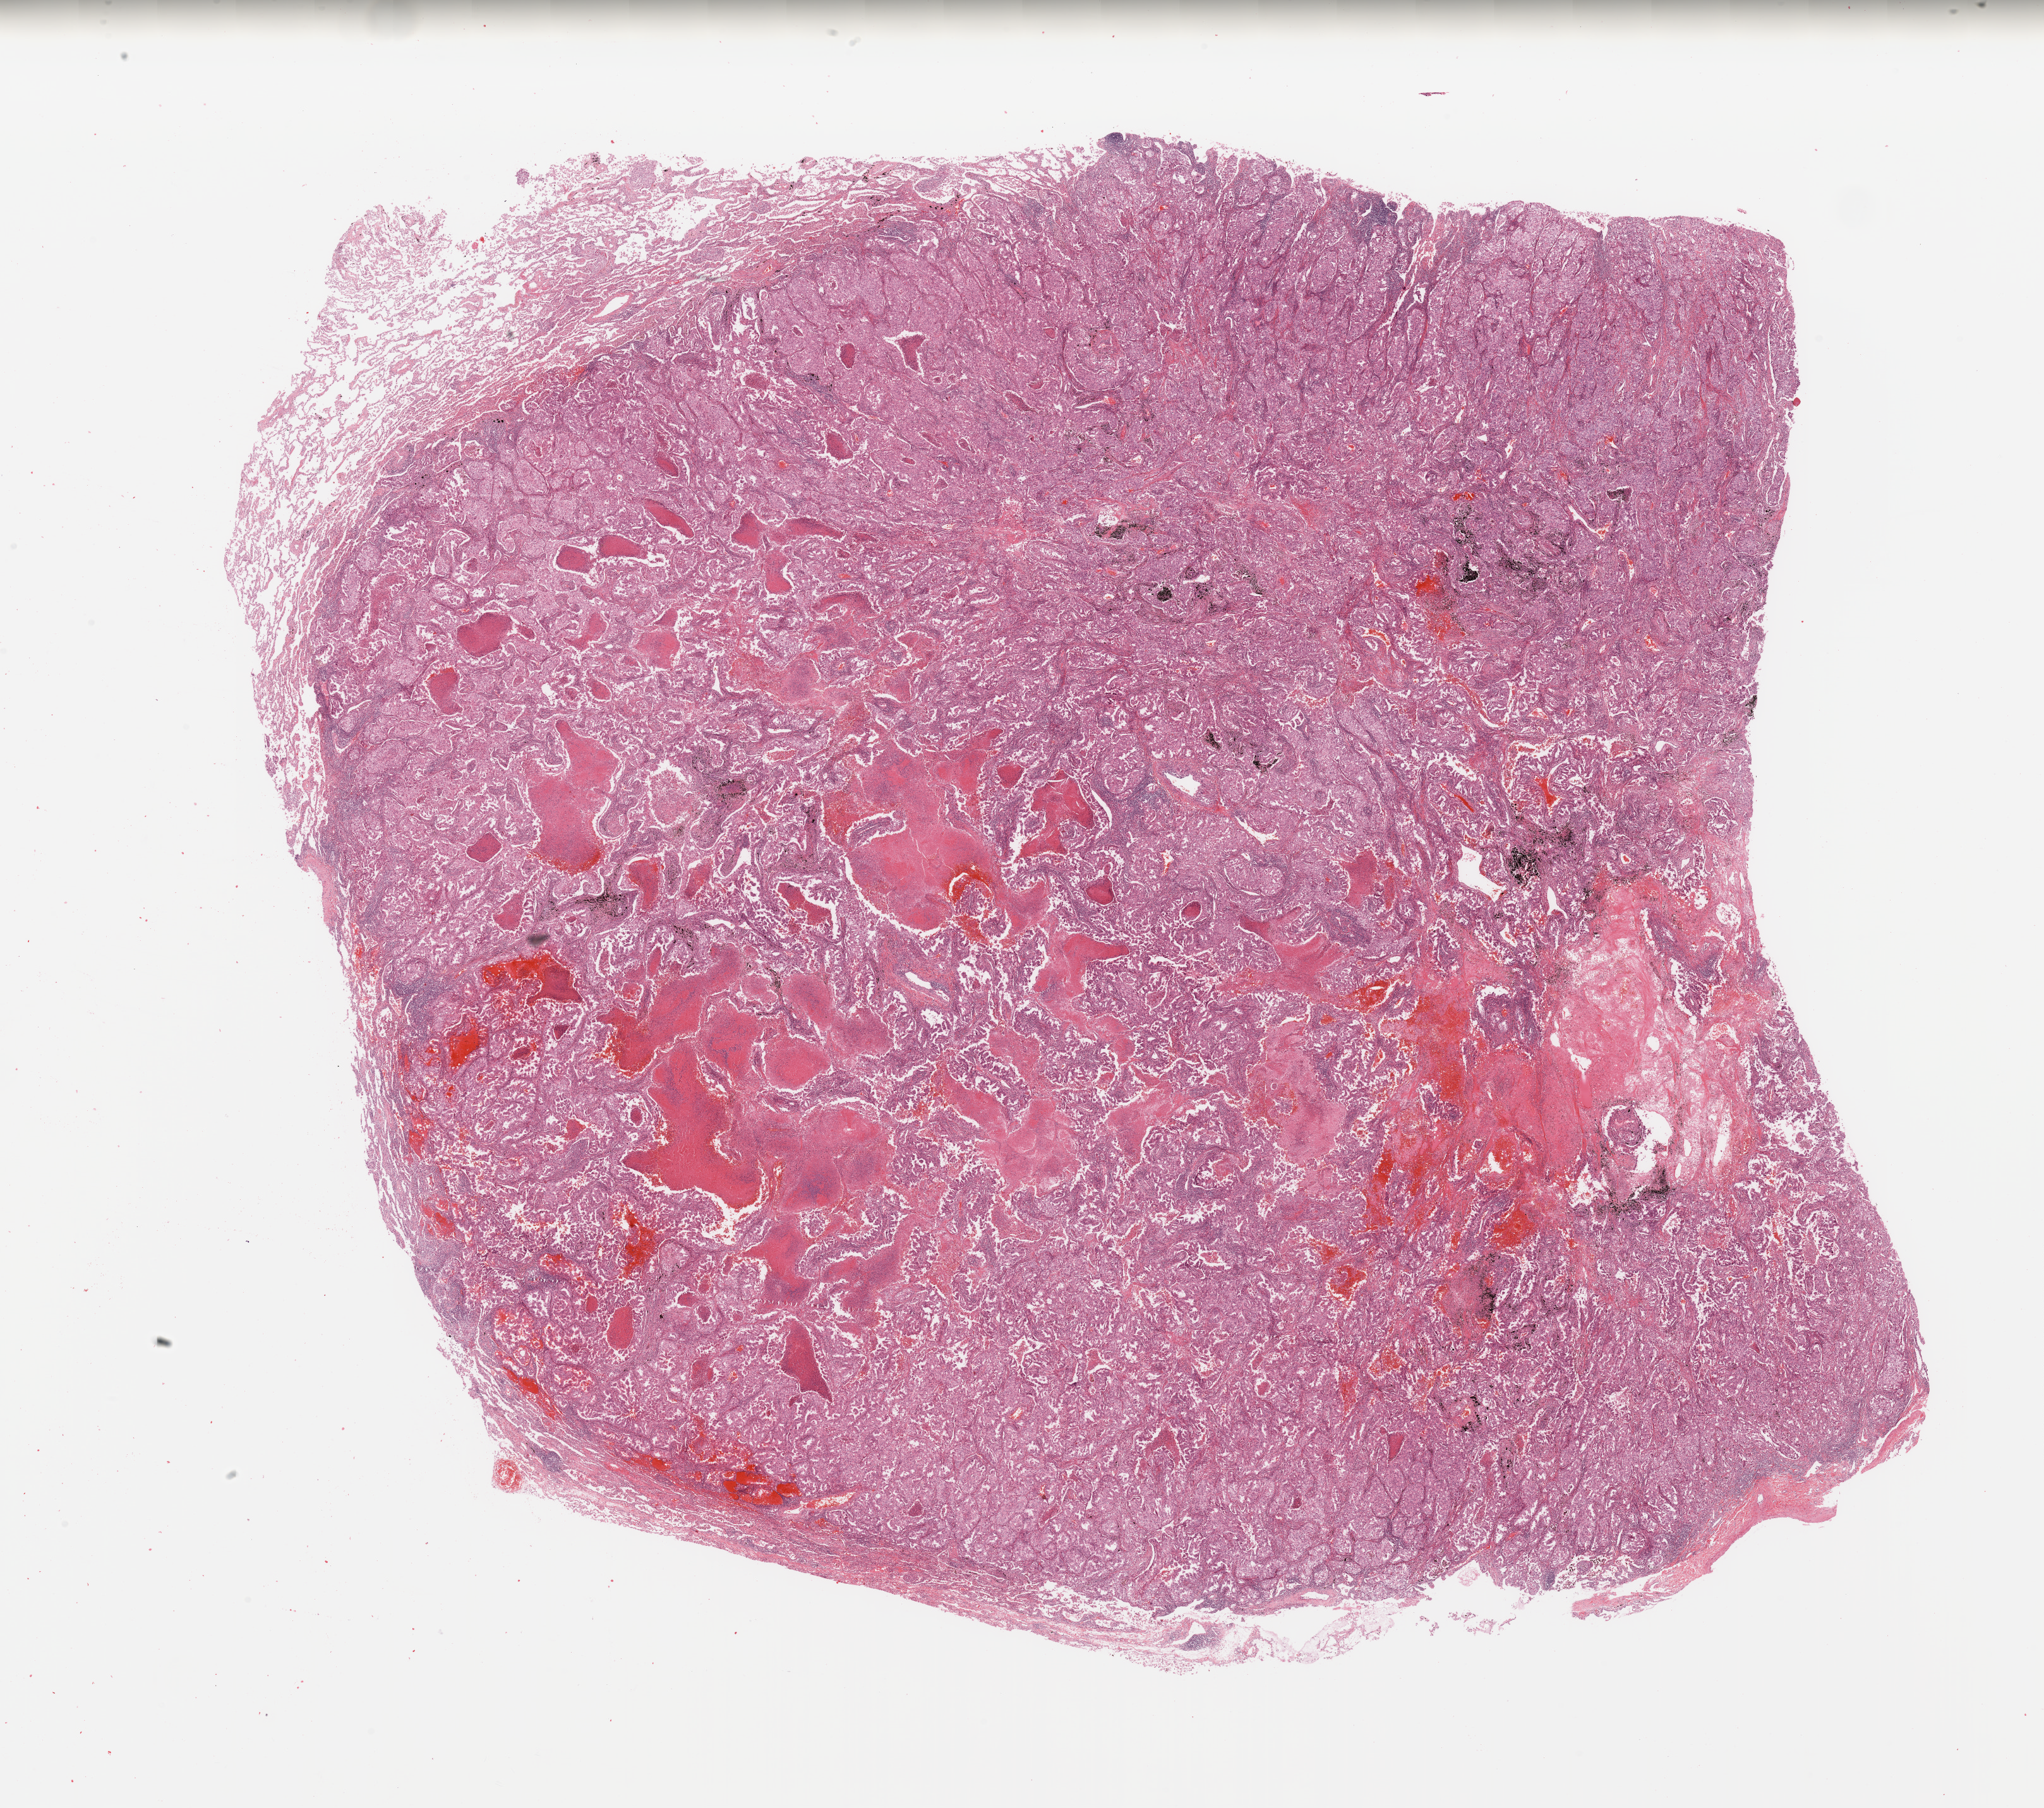
Digitized H&E tissue section (whole slide) — shown as a low-resolution overview of the whole scanned area (about 25.6 x 22.6 mm, from a 20x scan). Lung, tumour tissue. Male, 56 y/o. Histologic grade: G3 (poorly differentiated).
* AJCC pathologic stage: IB
* diagnosis: Adenocarcinoma, NOS